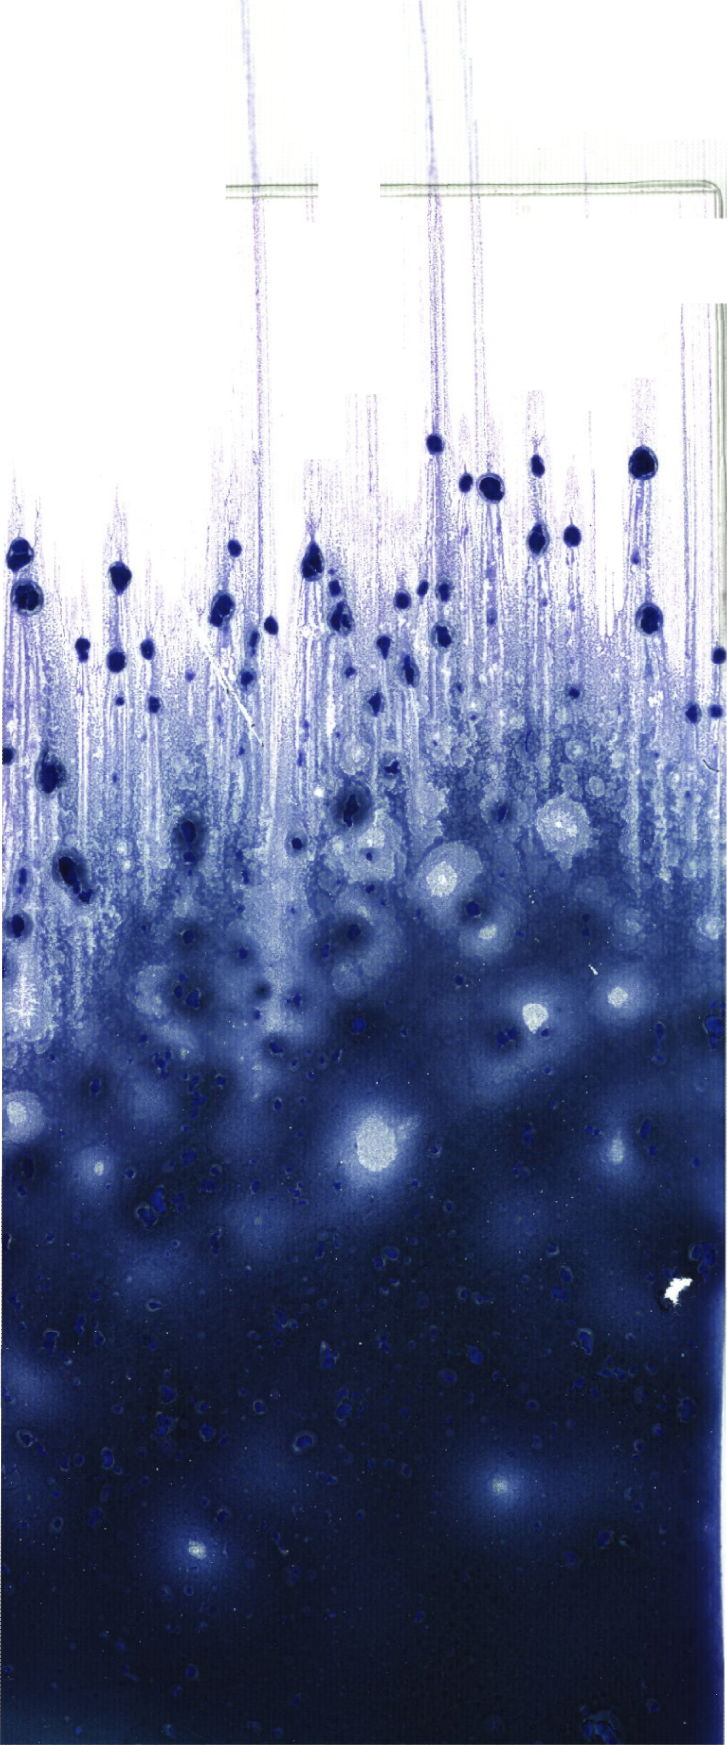
May-Grünwald-Giemsa (MGG)-stained marrow aspirate smear (whole slide) — whole scanned area (about 20.6 x 49.5 mm) shown as a low-resolution overview. Patient sex: male.
* diagnosis: B Acute Lymphoblastic Leukemia